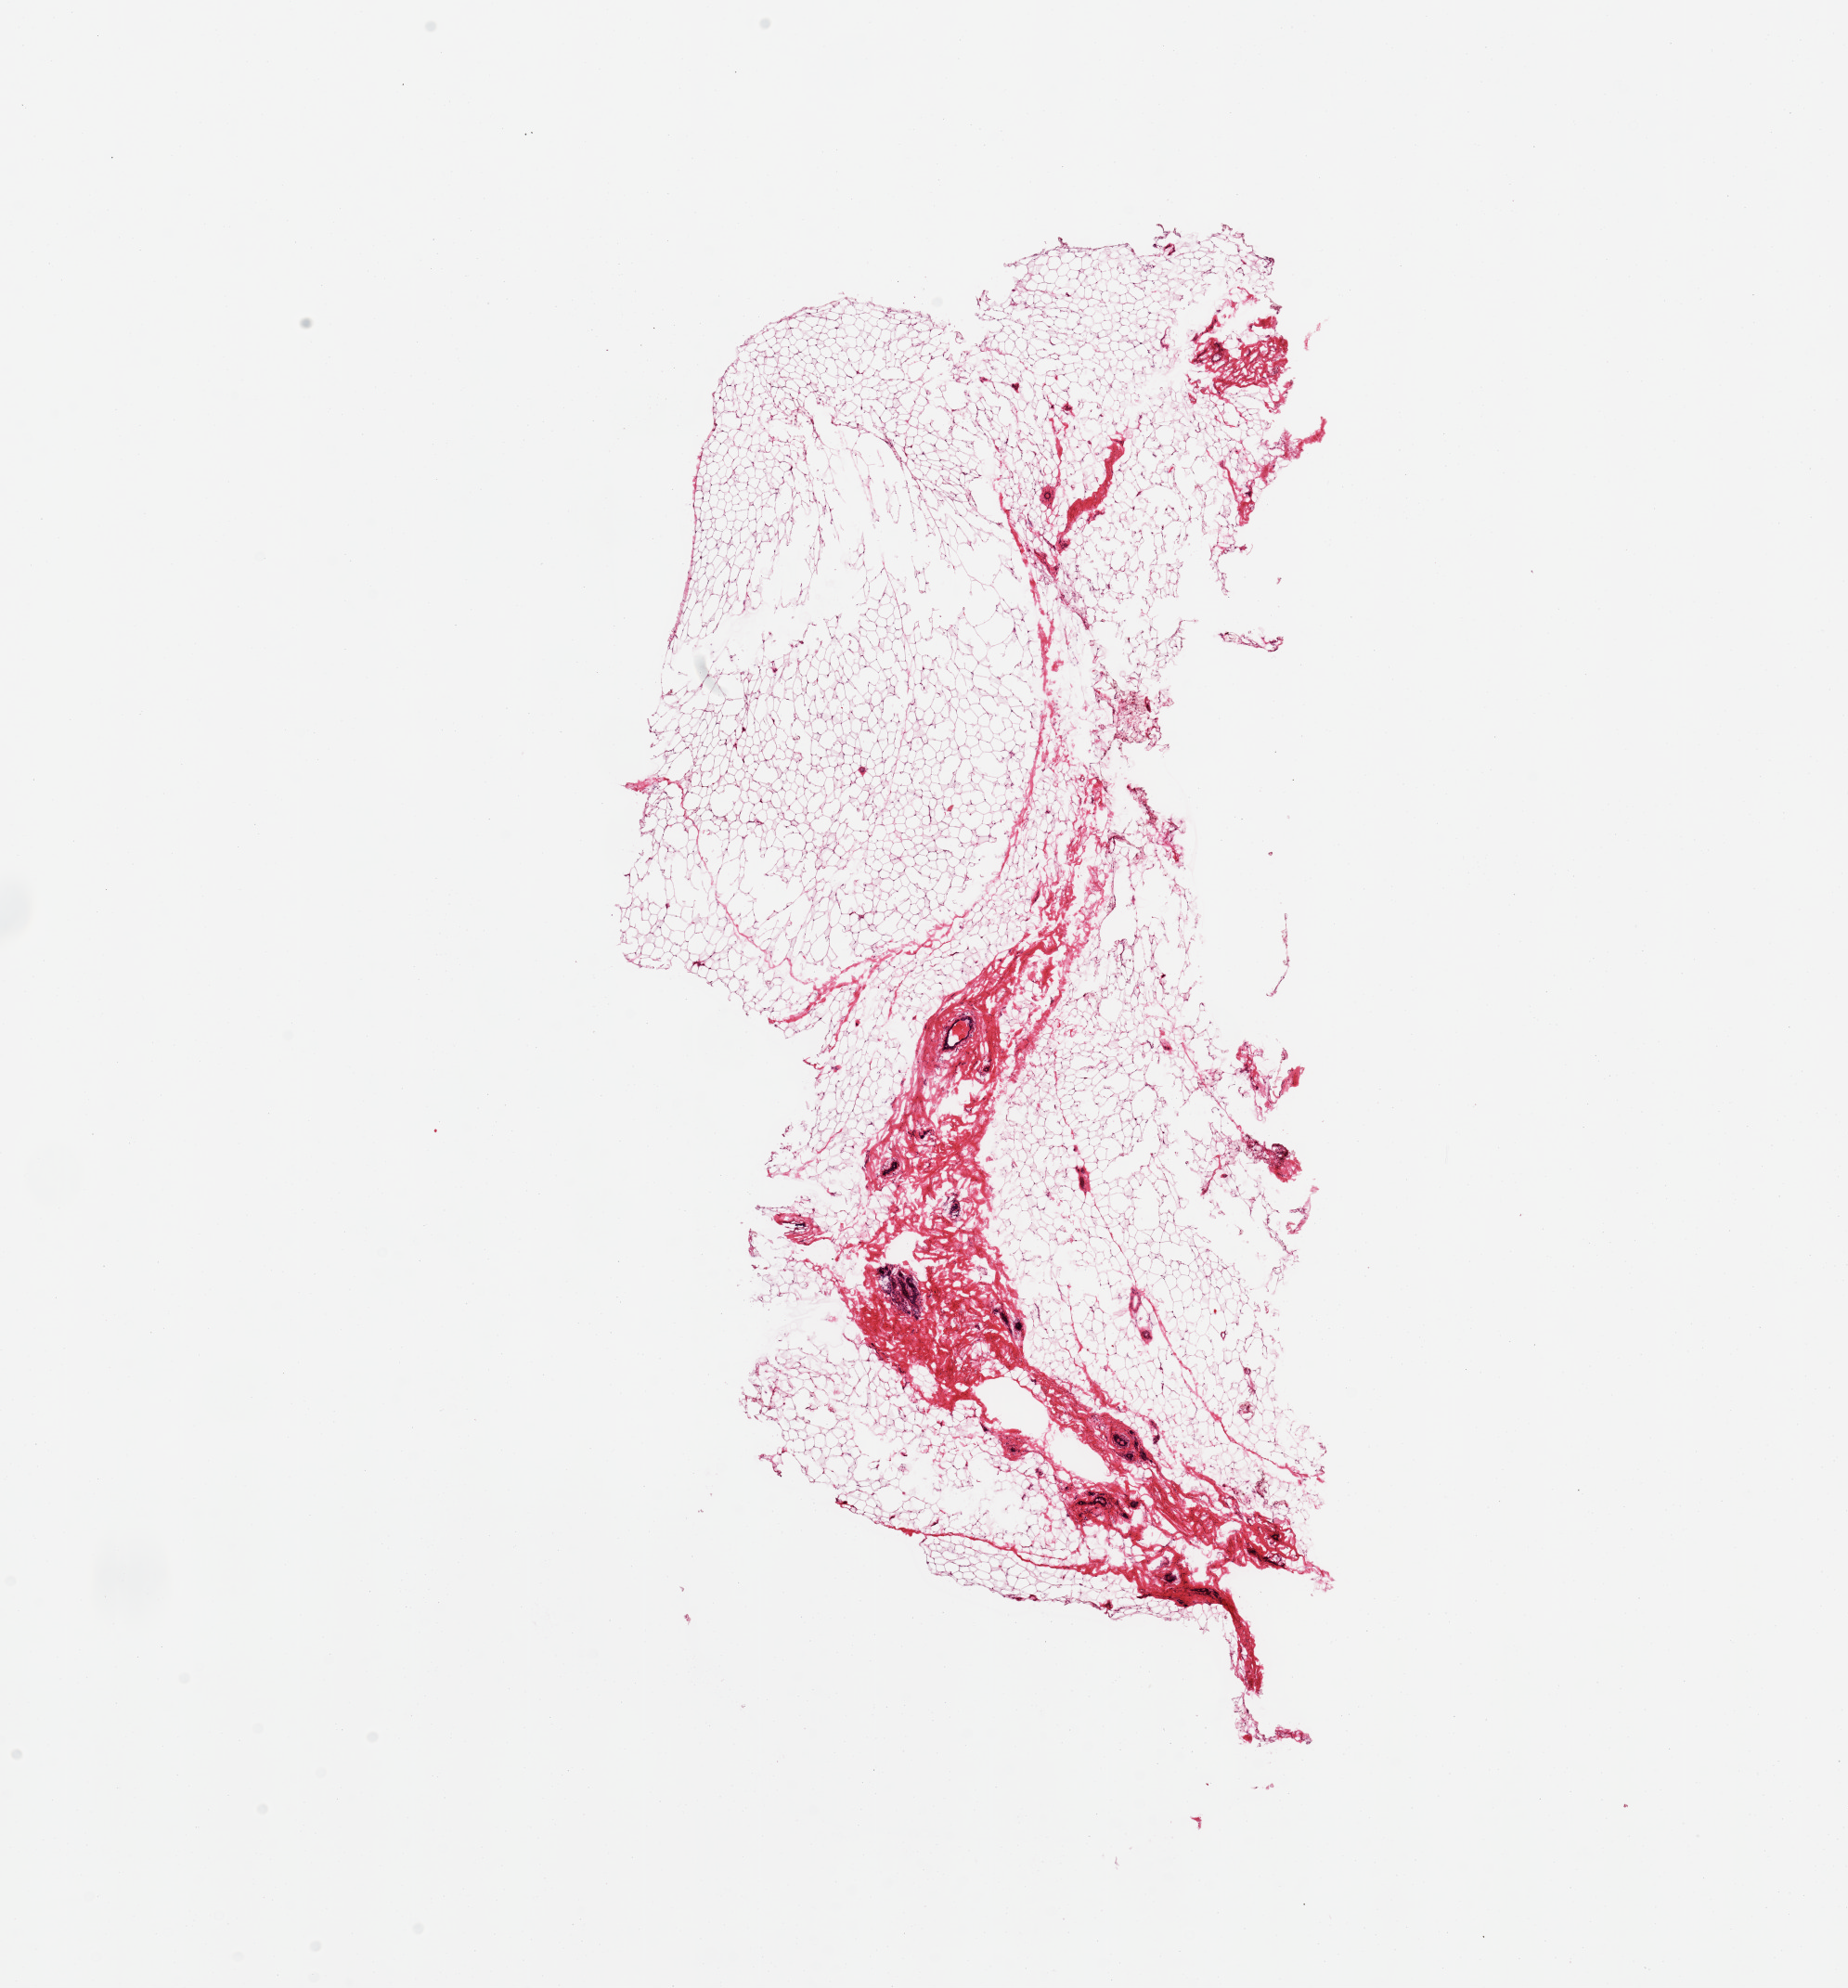
Haematoxylin and eosin whole-slide image, brightfield — a low-resolution overview of the entire scanned area, about 15.8 x 16.9 mm. Female donor.
Specimen: frozen section; target tissue: breast; tissue donor sample.